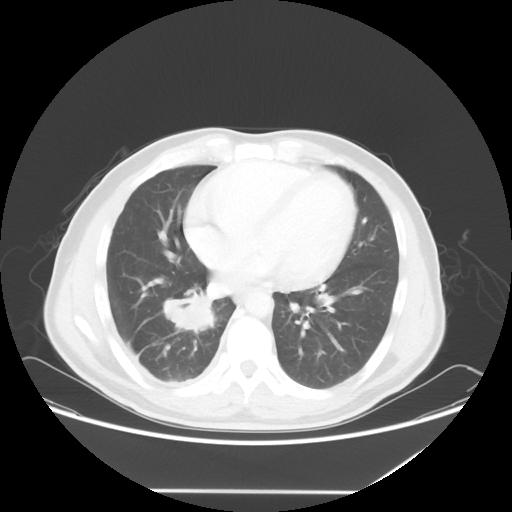
Chest CT, one axial slice. Reconstruction kernel STANDARD. 120 kVp. Lung window (W 1500 / L -600 HU). 5 mm slice thickness. 512 × 512 image matrix, field of view 419 × 419 mm. Male patient, age 48 years. Case-level facts recorded for this patient, not image findings: clinical TNM (as recorded): T3 N3 M1a.
Outlined on this slice (rectangle marked by the reading radiologist):
- lung tumour (recorded histology: squamous cell carcinoma): bounding box [x1, y1, x2, y2] px = [158, 287, 220, 337]